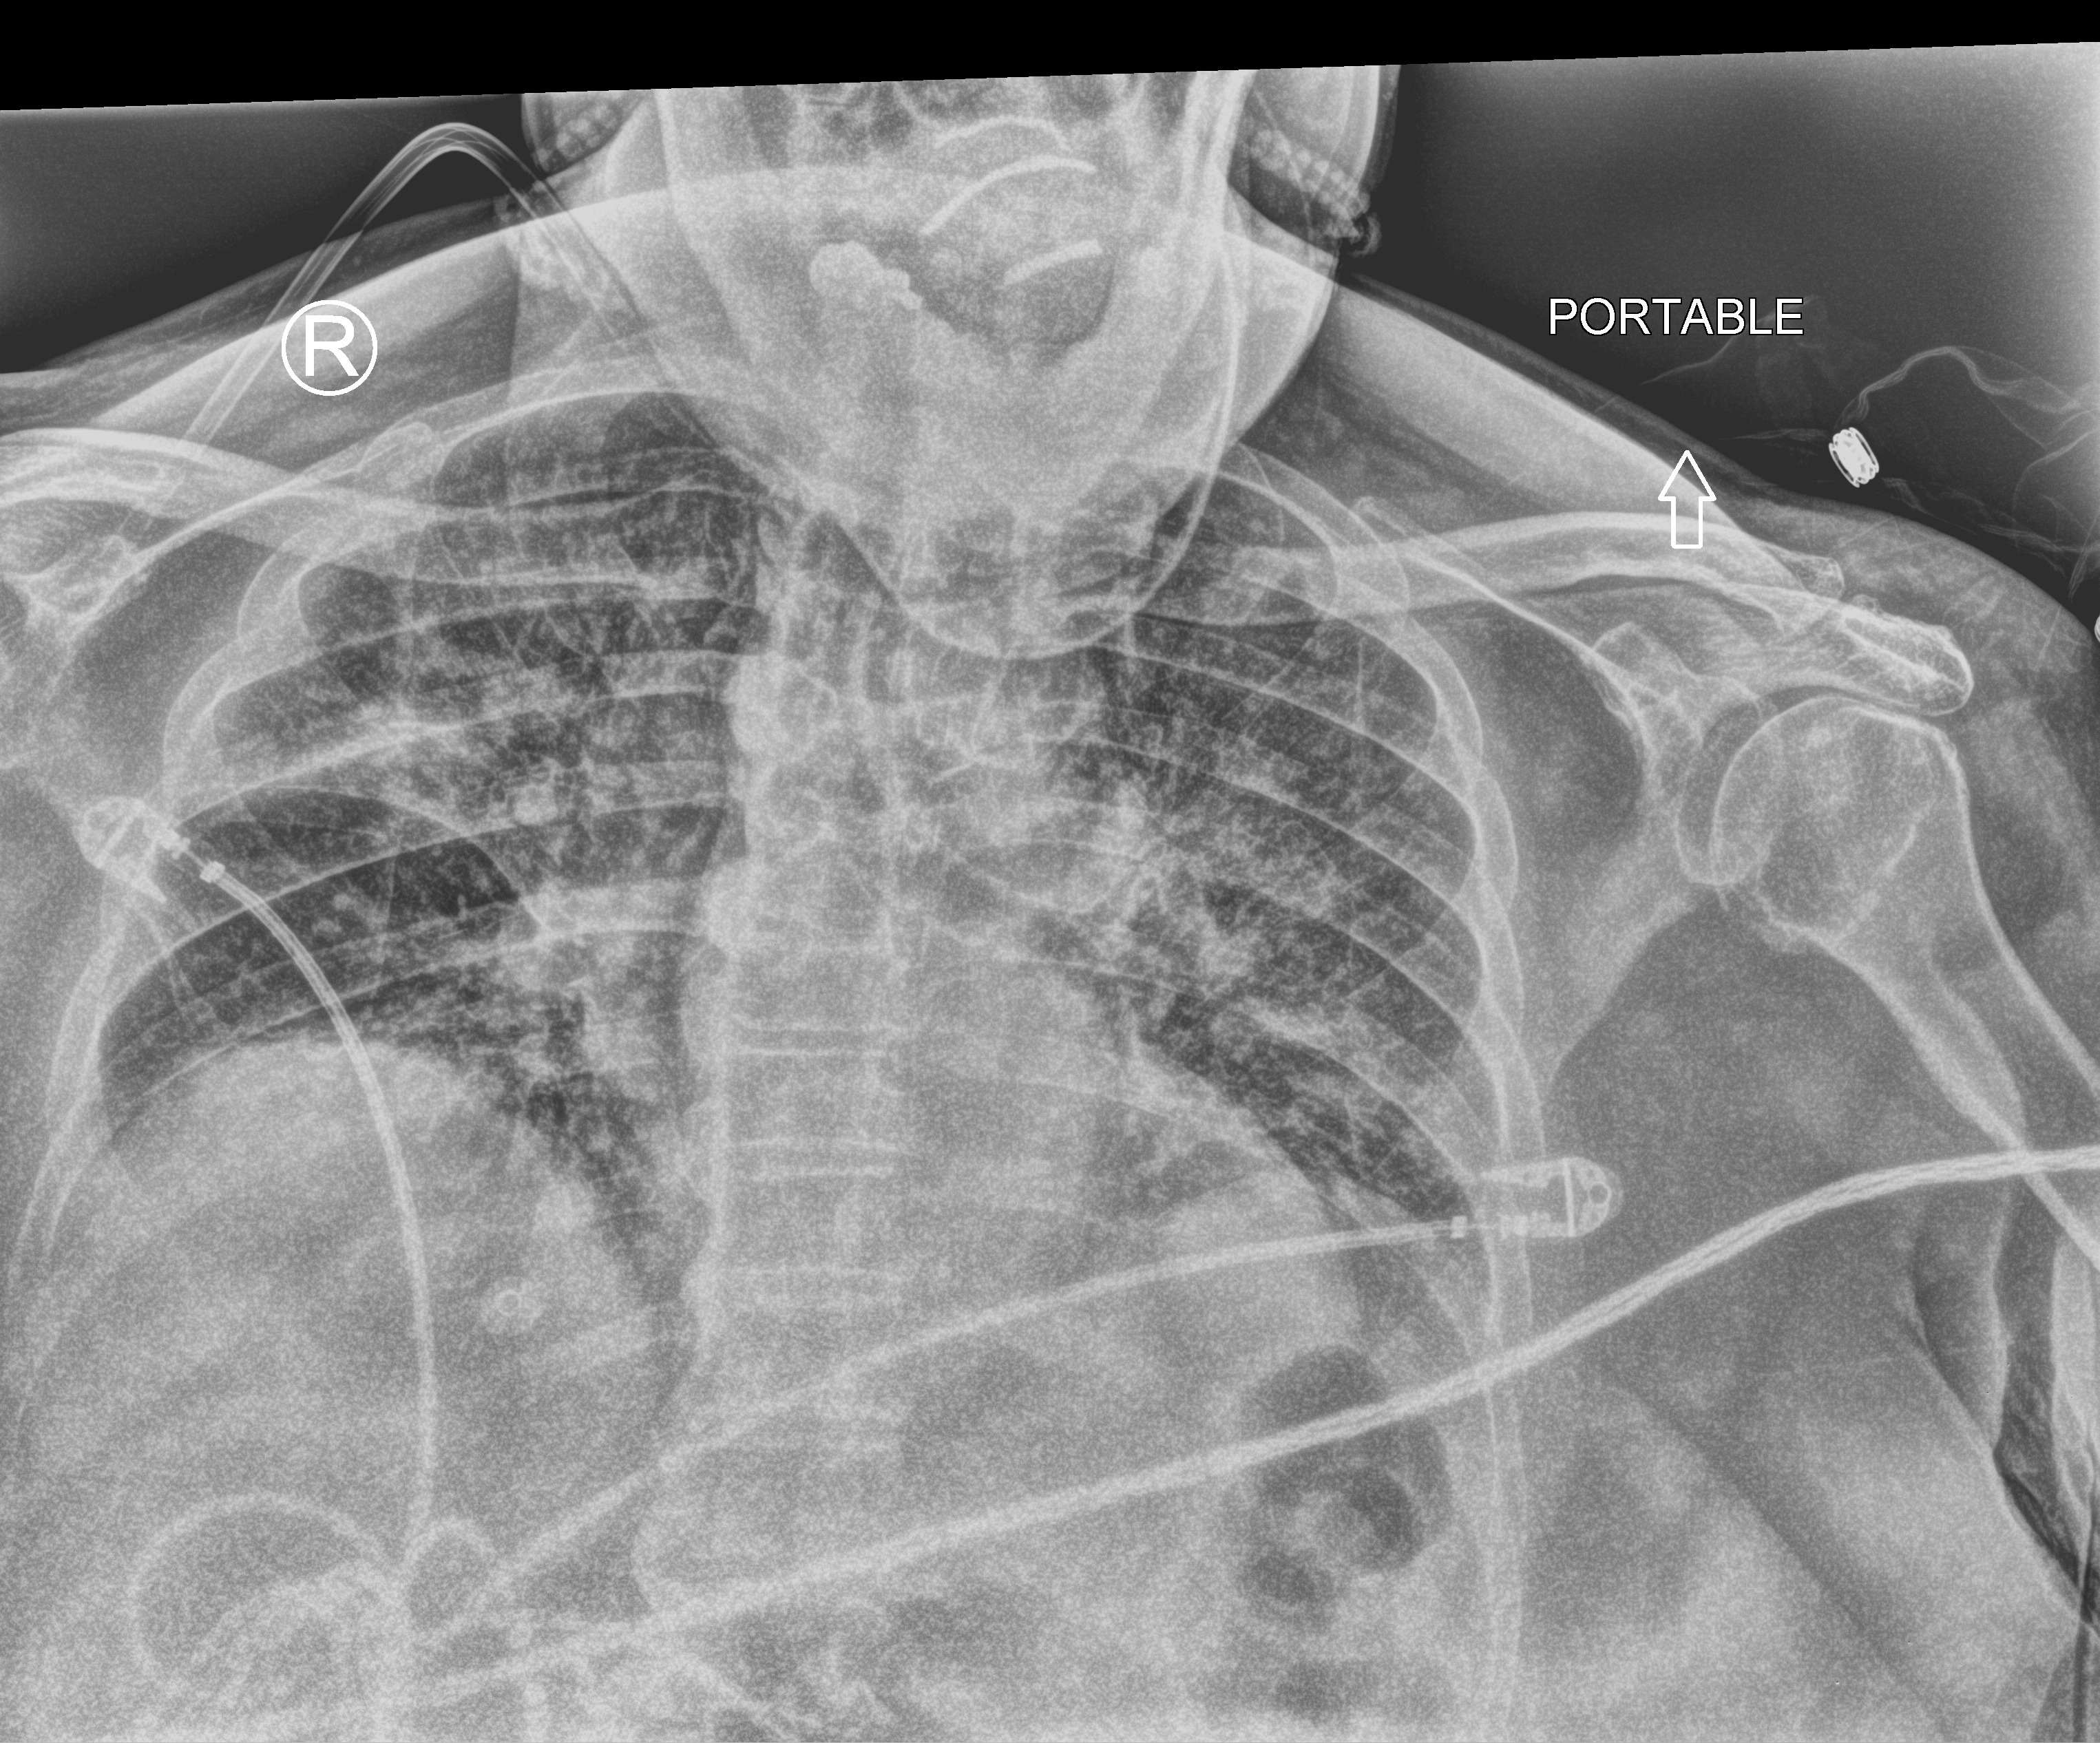
Bedside chest radiograph (computed radiography), anteroposterior (AP) projection. Female patient hospitalised with COVID-19, age 75–90 years.
Hospital-stay facts (about this admission, not read from this image; timing relative to this image not recorded): COPD (admission record): no.